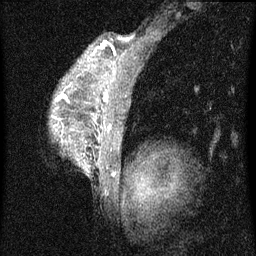
Breast MRI (dynamic contrast-enhanced), one sagittal slice; dynamic contrast-enhanced series, image 2 of 4 at this slice position (ordered by acquisition); 1.5 T; TE 4.2 ms, TR 8 ms; 2 mm slice thickness; 256 × 256 image matrix. Patient: female, 50 years.
Annotated regions visible in this slice (semi-automatic segmentation, software-assisted and operator-edited):
- analysis volume of interest (the breast-tissue region the enhancement analysis was run in; not a lesion): bounding box <53,52,124,175> (left, top, right, bottom; pixels)
- tumour enhancement mask (voxels above the 70 % enhancement threshold inside the analysis volume of interest): <59,96,109,103>